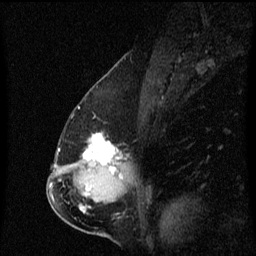
Breast MRI (dynamic contrast-enhanced), one sagittal slice. Slice 33 of 60 in the series (ordered by position). Dynamic contrast-enhanced series, image 2 of 3 at this slice position (ordered by acquisition). 1.5 T. TE 4.2 ms, TR 8.4 ms. 256 × 256 image matrix. Patient: female, 57 years. From the clinical record (not read from this slice): setting: breast cancer imaged before/during neoadjuvant chemotherapy; receptor status: HR-positive, HER2-negative.
Annotated regions visible in this slice (semi-automatic segmentation, software-assisted and operator-edited):
- analysis volume of interest (the breast-tissue region the enhancement analysis was run in; not a lesion): bounding box <66,134,129,177> (left, top, right, bottom; pixels)
- tumour enhancement mask (voxels above the 70 % enhancement threshold inside the analysis volume of interest): <83,134,122,177>